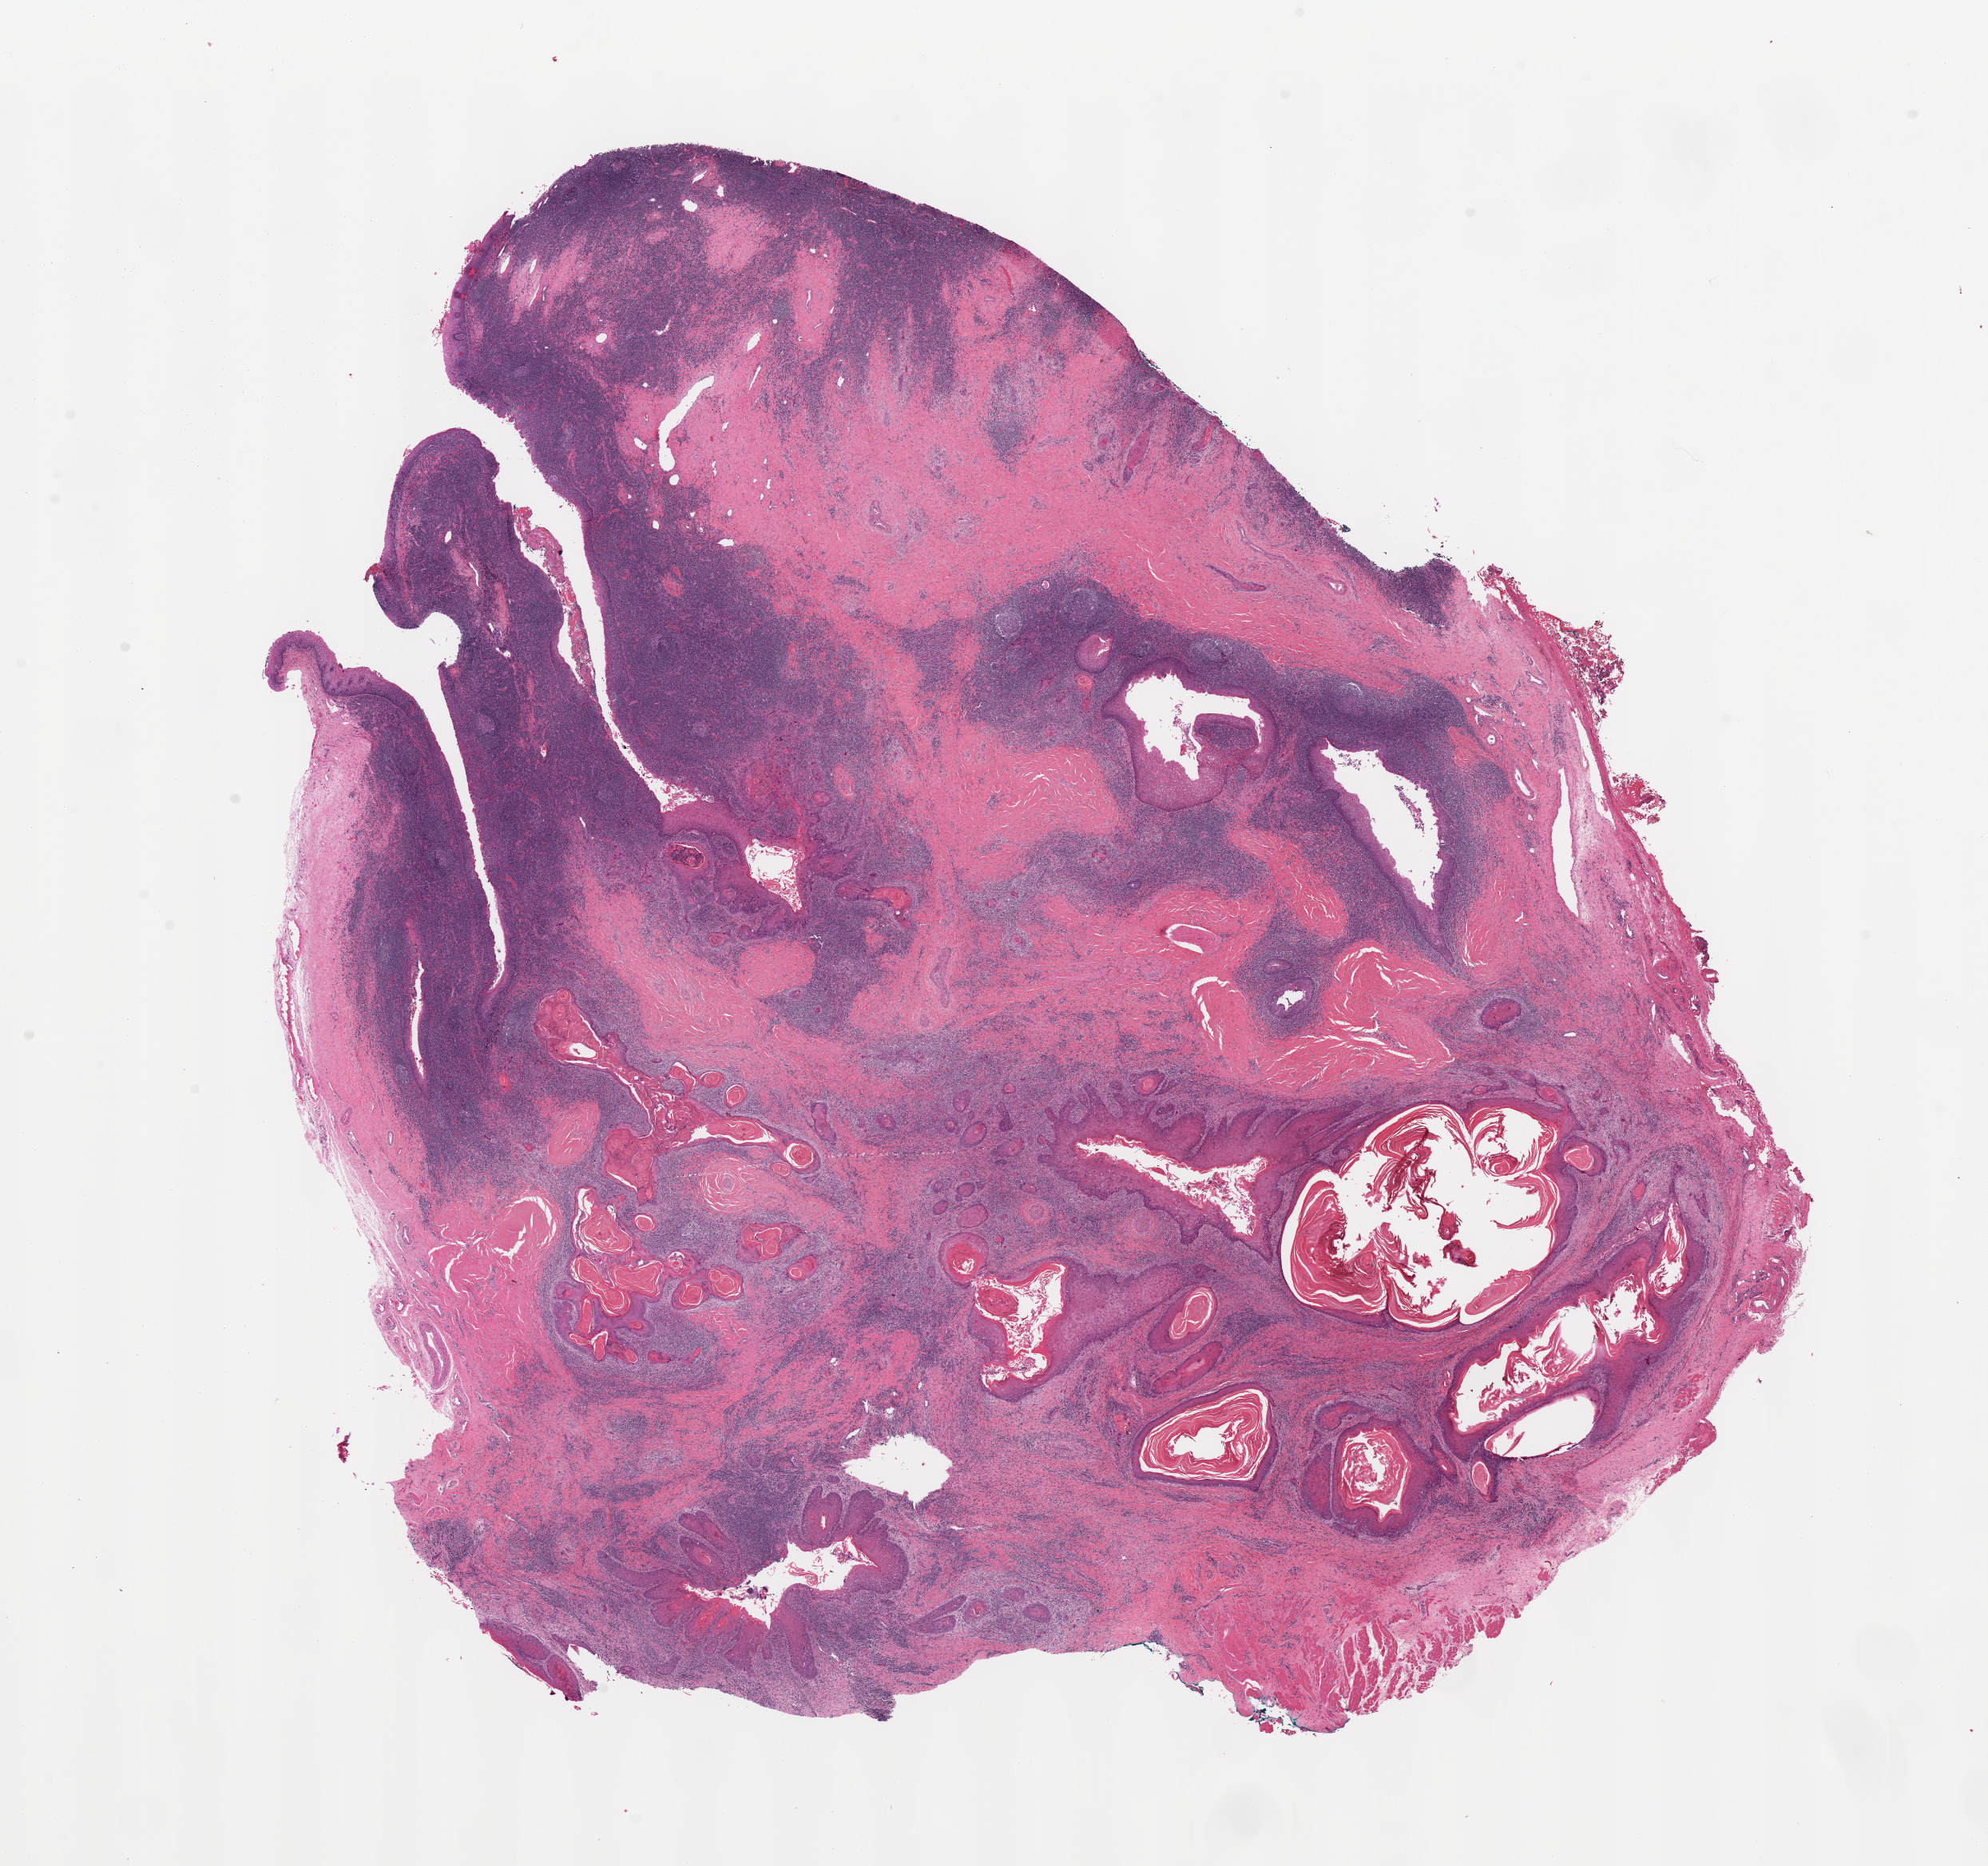
Digitized Hematoxylin and eosin (H&E) stained tissue section (whole slide) — low-resolution overview of the scanned area, about 19.7 x 18.5 mm (slide scanned at 20x), head and neck, tissue type not recorded. 56-year-old male patient.
• patient diagnosis: Squamous cell carcinoma, NOS (cheek mucosa)